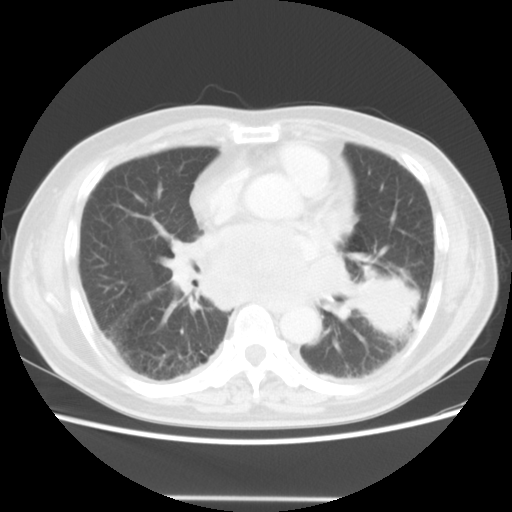
Chest CT, one axial slice. Position 24 of 56 along the scan axis. Lung window (W 1500 / L -600 HU). 512 × 512 image matrix, field of view 360 × 360 mm. Patient: male, 66 years. Case-level facts recorded for this patient, not image findings: clinical TNM (as recorded): T4 N3 M0; histopathological grade: G3.
Outlined on this slice (rectangle marked by the reading radiologist):
- lung tumour (recorded histology: small cell carcinoma): bounding box <347,262,425,353> (left, top, right, bottom; pixels)